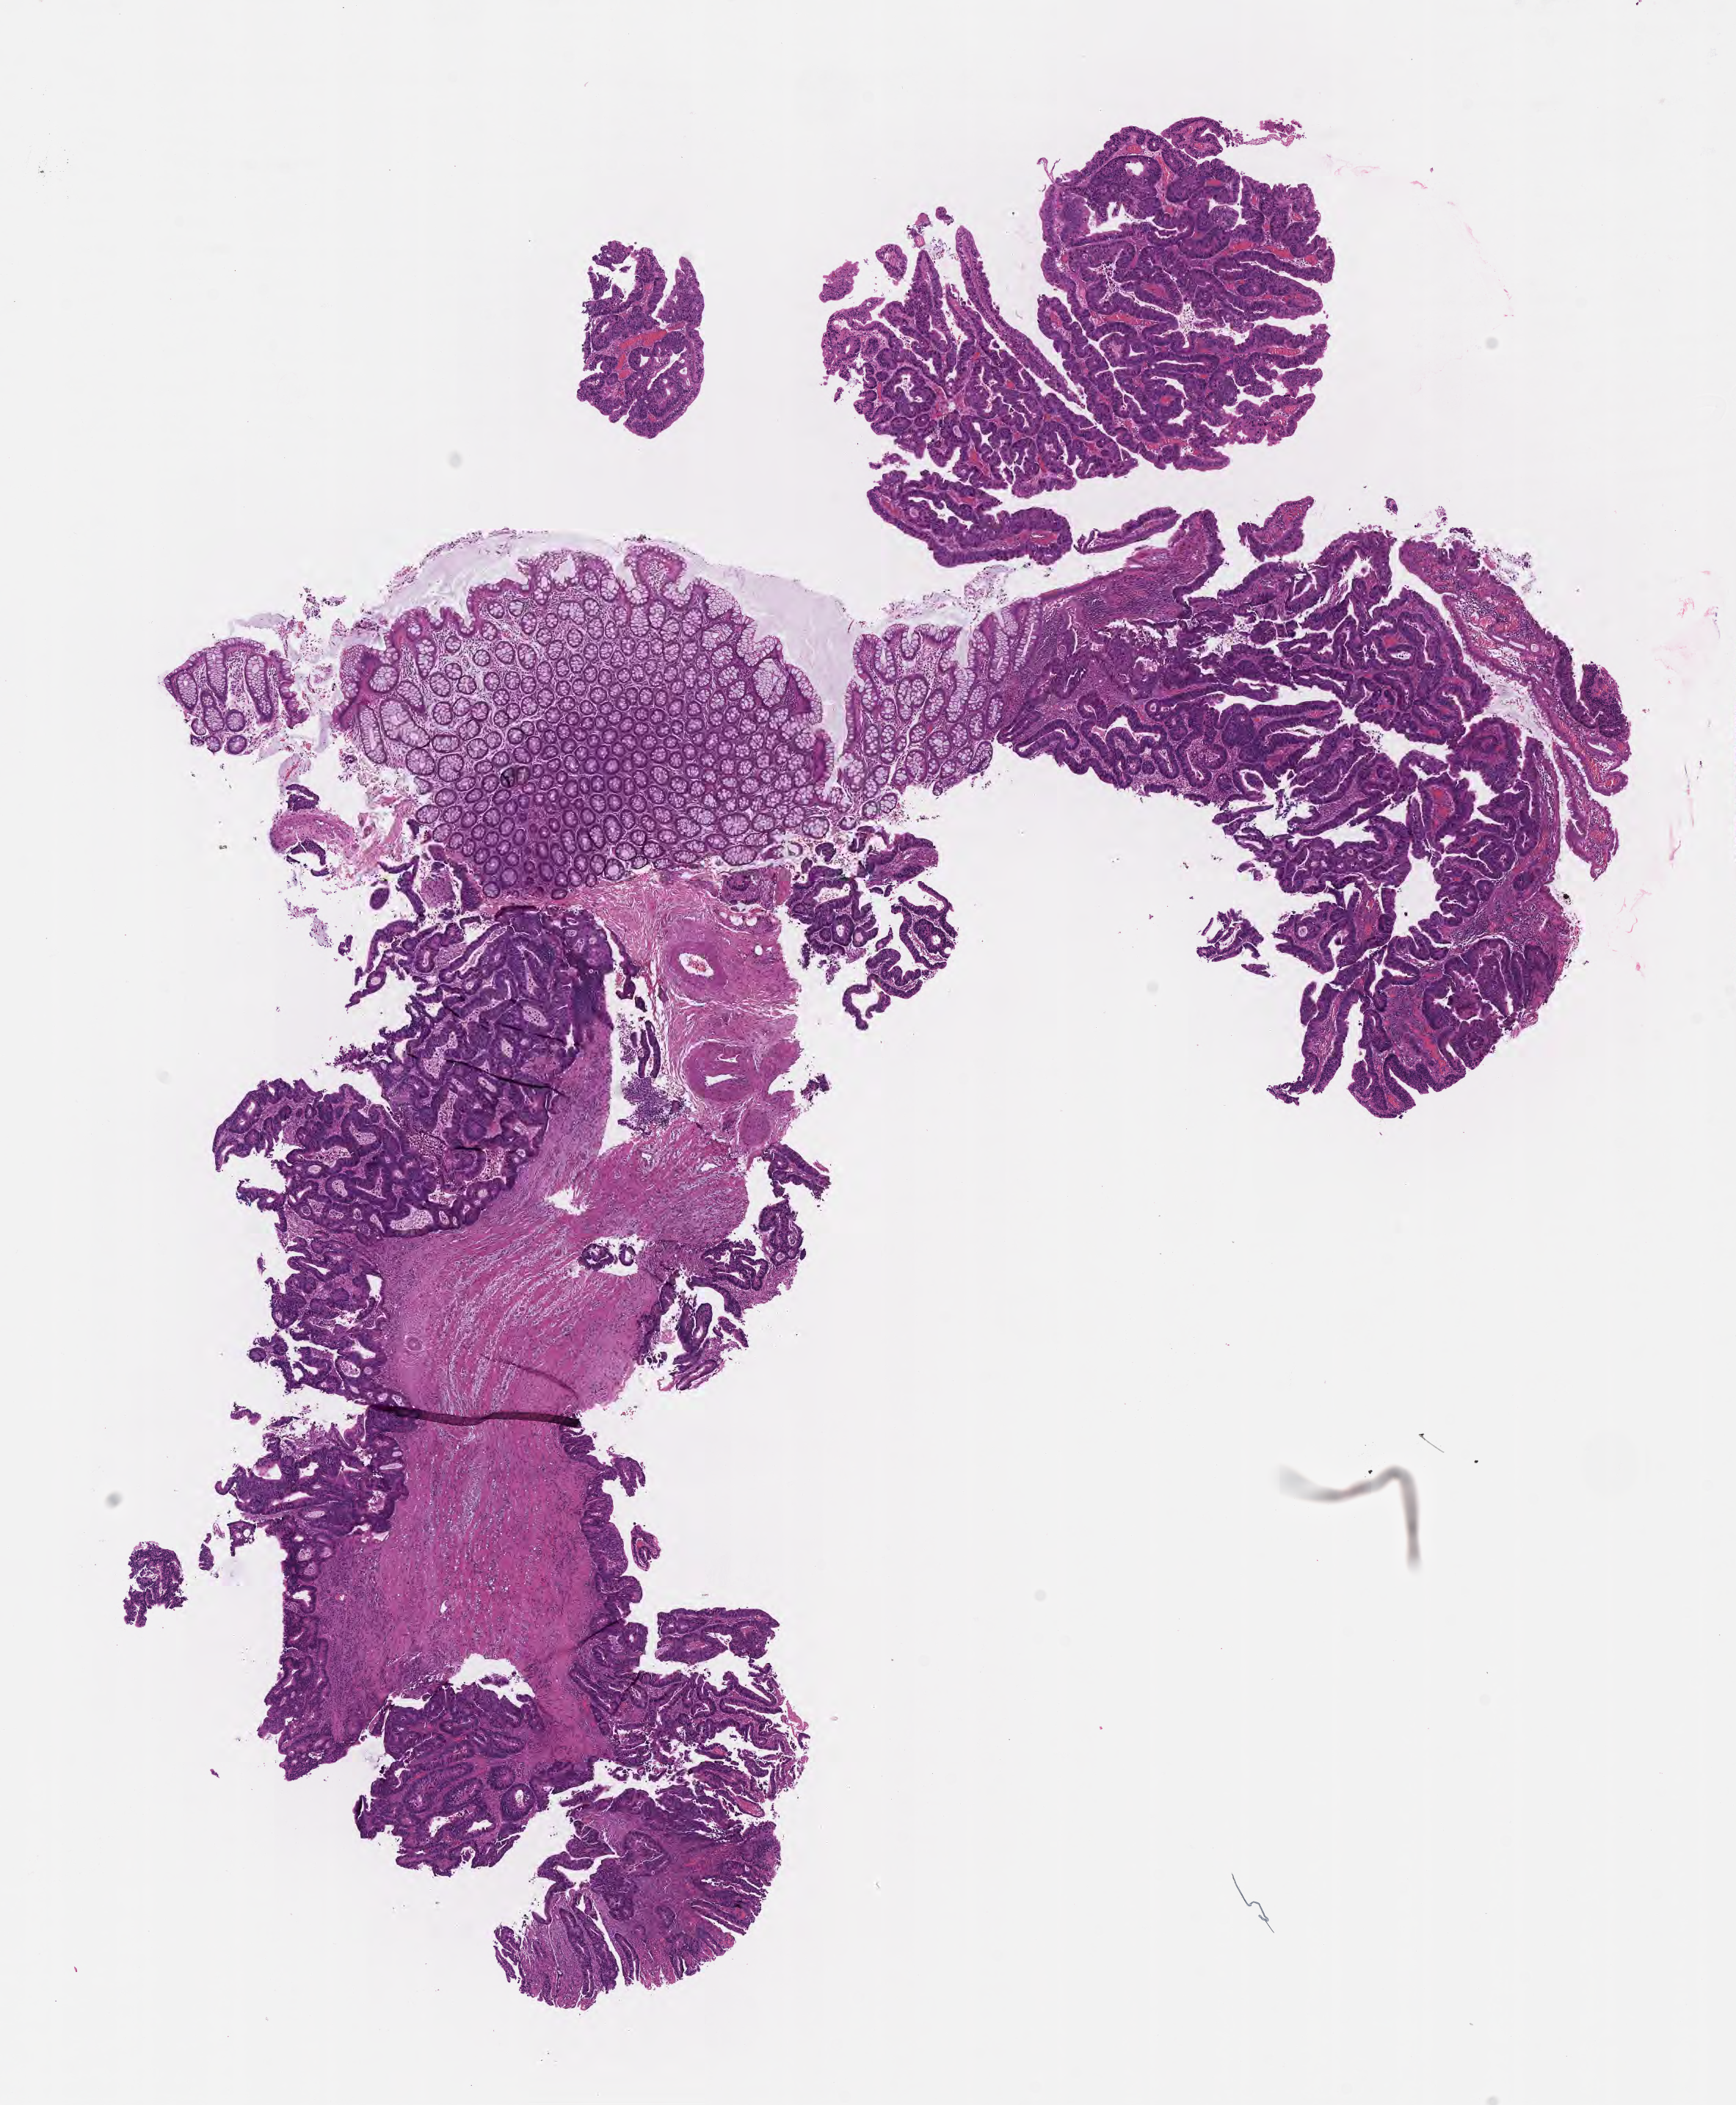
Hematoxylin and eosin (H&E) whole-slide image — a low-resolution overview of the entire scanned area, about 9.6 x 11.6 mm, formalin-fixed, paraffin-embedded (FFPE) tissue, primary tumor, site: sigmoid colon. Female, age 72 years at initial diagnosis. Tumor grade: G2 (moderately differentiated). Pathologist review of this section (percent, as recorded): tumor cells 80%, tumor nuclei 80%, stromal cells 17%, necrosis 0%, normal cells 3%. Infiltration values recorded for this section: lymphocyte infiltration 4%, monocyte infiltration 1%, neutrophil infiltration 7%.
Histologic diagnosis: Adenocarcinoma, NOS. Section: top of the tissue portion. AJCC pathologic stage: Stage IIA.